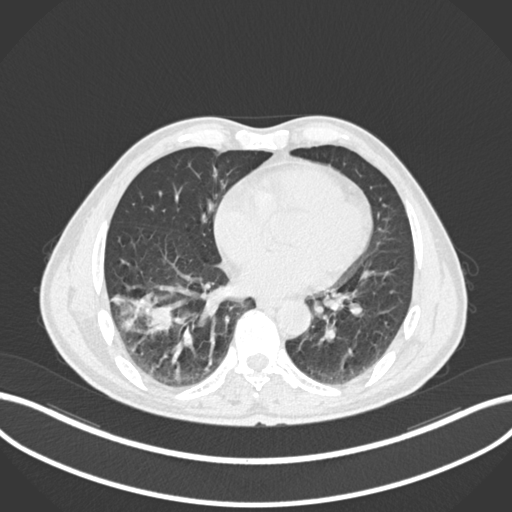
Chest CT, one axial slice; slice 68 of 208 in the series (ordered by position); reconstruction kernel B30f; 120 kVp; lung window (W 1500 / L -600 HU); 512 × 512 image matrix, field of view 400 × 400 mm. Patient: male, 58 years. Case-level facts recorded for this patient, not image findings: clinical TNM (as recorded): T3 N0 M0; histopathological grade: G2.
Structures marked on this image (rectangle marked by the reading radiologist):
- lung tumour (recorded histology: squamous cell carcinoma): box from (x=105, y=291) to (x=179, y=343) px